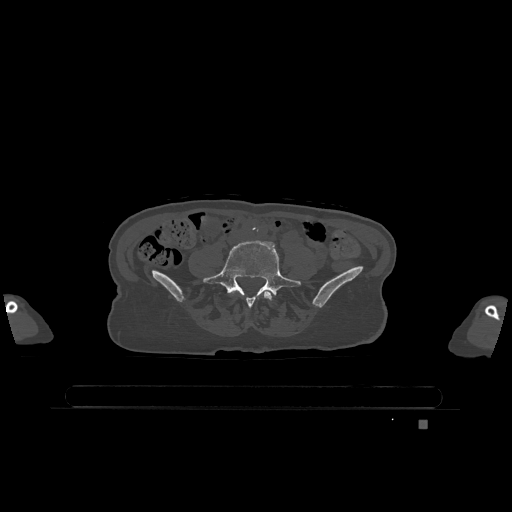
CT including the spine, one axial slice. Slice 251 of 1317 in the series (ordered by position). Bone window (W 1800 / L 400 HU). 512 × 512 image matrix, field of view 500 × 500 mm. Female patient, age 74 years. Case-level facts recorded for this patient, not image findings: primary cancer: lung.
Annotated regions visible in this slice (semi-automatic segmentation, software-assisted and operator-edited):
- L4 vertebra: bounding box [x1, y1, x2, y2] px = [232, 291, 272, 301]
- L5 vertebra: [204, 240, 301, 306]